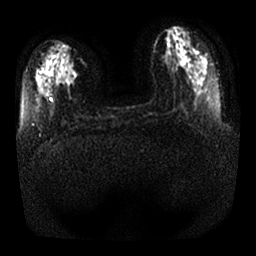
Breast MRI, one axial slice; position 10 of 25 along the scan axis; diffusion-weighted series; image 2 of 4 stored at this slice position (different b-values; order by instance number); 1.5 T; 4 mm slice thickness; 256 × 256 image matrix, field of view 350 × 350 mm. Female patient.
Outlined on this slice (outlined manually by an expert reader):
- tumour on diffusion-weighted imaging: bounding box <60,62,76,84> (left, top, right, bottom; pixels)